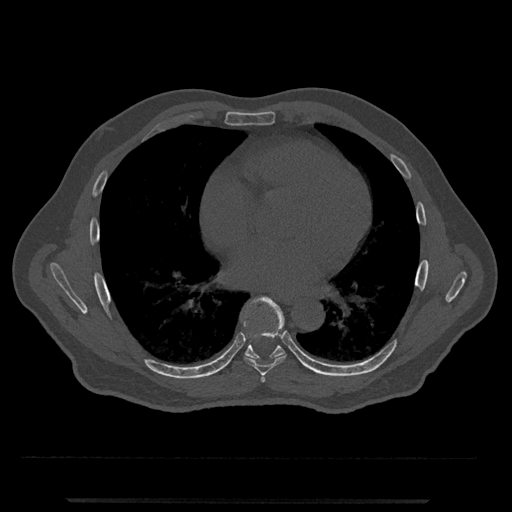
CT including the spine, one axial slice; position 660 of 797 along the scan axis; reconstruction kernel Br40s/3; 120 kVp; bone window (W 1800 / L 400 HU); 512 × 512 image matrix. Patient: male, 63 years. From the clinical record (not read from this slice): primary cancer: prostate.
Structures marked on this image (semi-automatically segmented with operator editing):
- T6 vertebra: box from (x=261, y=375) to (x=265, y=383) px
- T7 vertebra: (x=244, y=297)–(x=286, y=375)
- T8 vertebra: (x=245, y=333)–(x=285, y=359)